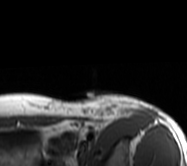
MRI of an extremity soft-tissue mass, one axial slice. Position 49 of 62 along the scan axis. MR volume resampled by the dataset authors to the PET/CT grid (not the native acquisition matrix). 3.27 mm slice thickness. 187 × 166 image matrix, field of view 183 × 162 mm. Female patient. Case-level facts recorded for this patient, not image findings: histological type: leiomyosarcoma; grade: high; site of the primary tumour: groin.
Structures marked on this image (expert contour drawn on MRI and transferred to this co-registered scan by the dataset authors):
- gross tumour volume including surrounding oedema: bounding box <89,94,158,121> (left, top, right, bottom; pixels)
- gross tumour volume (mass): <91,108,113,120>